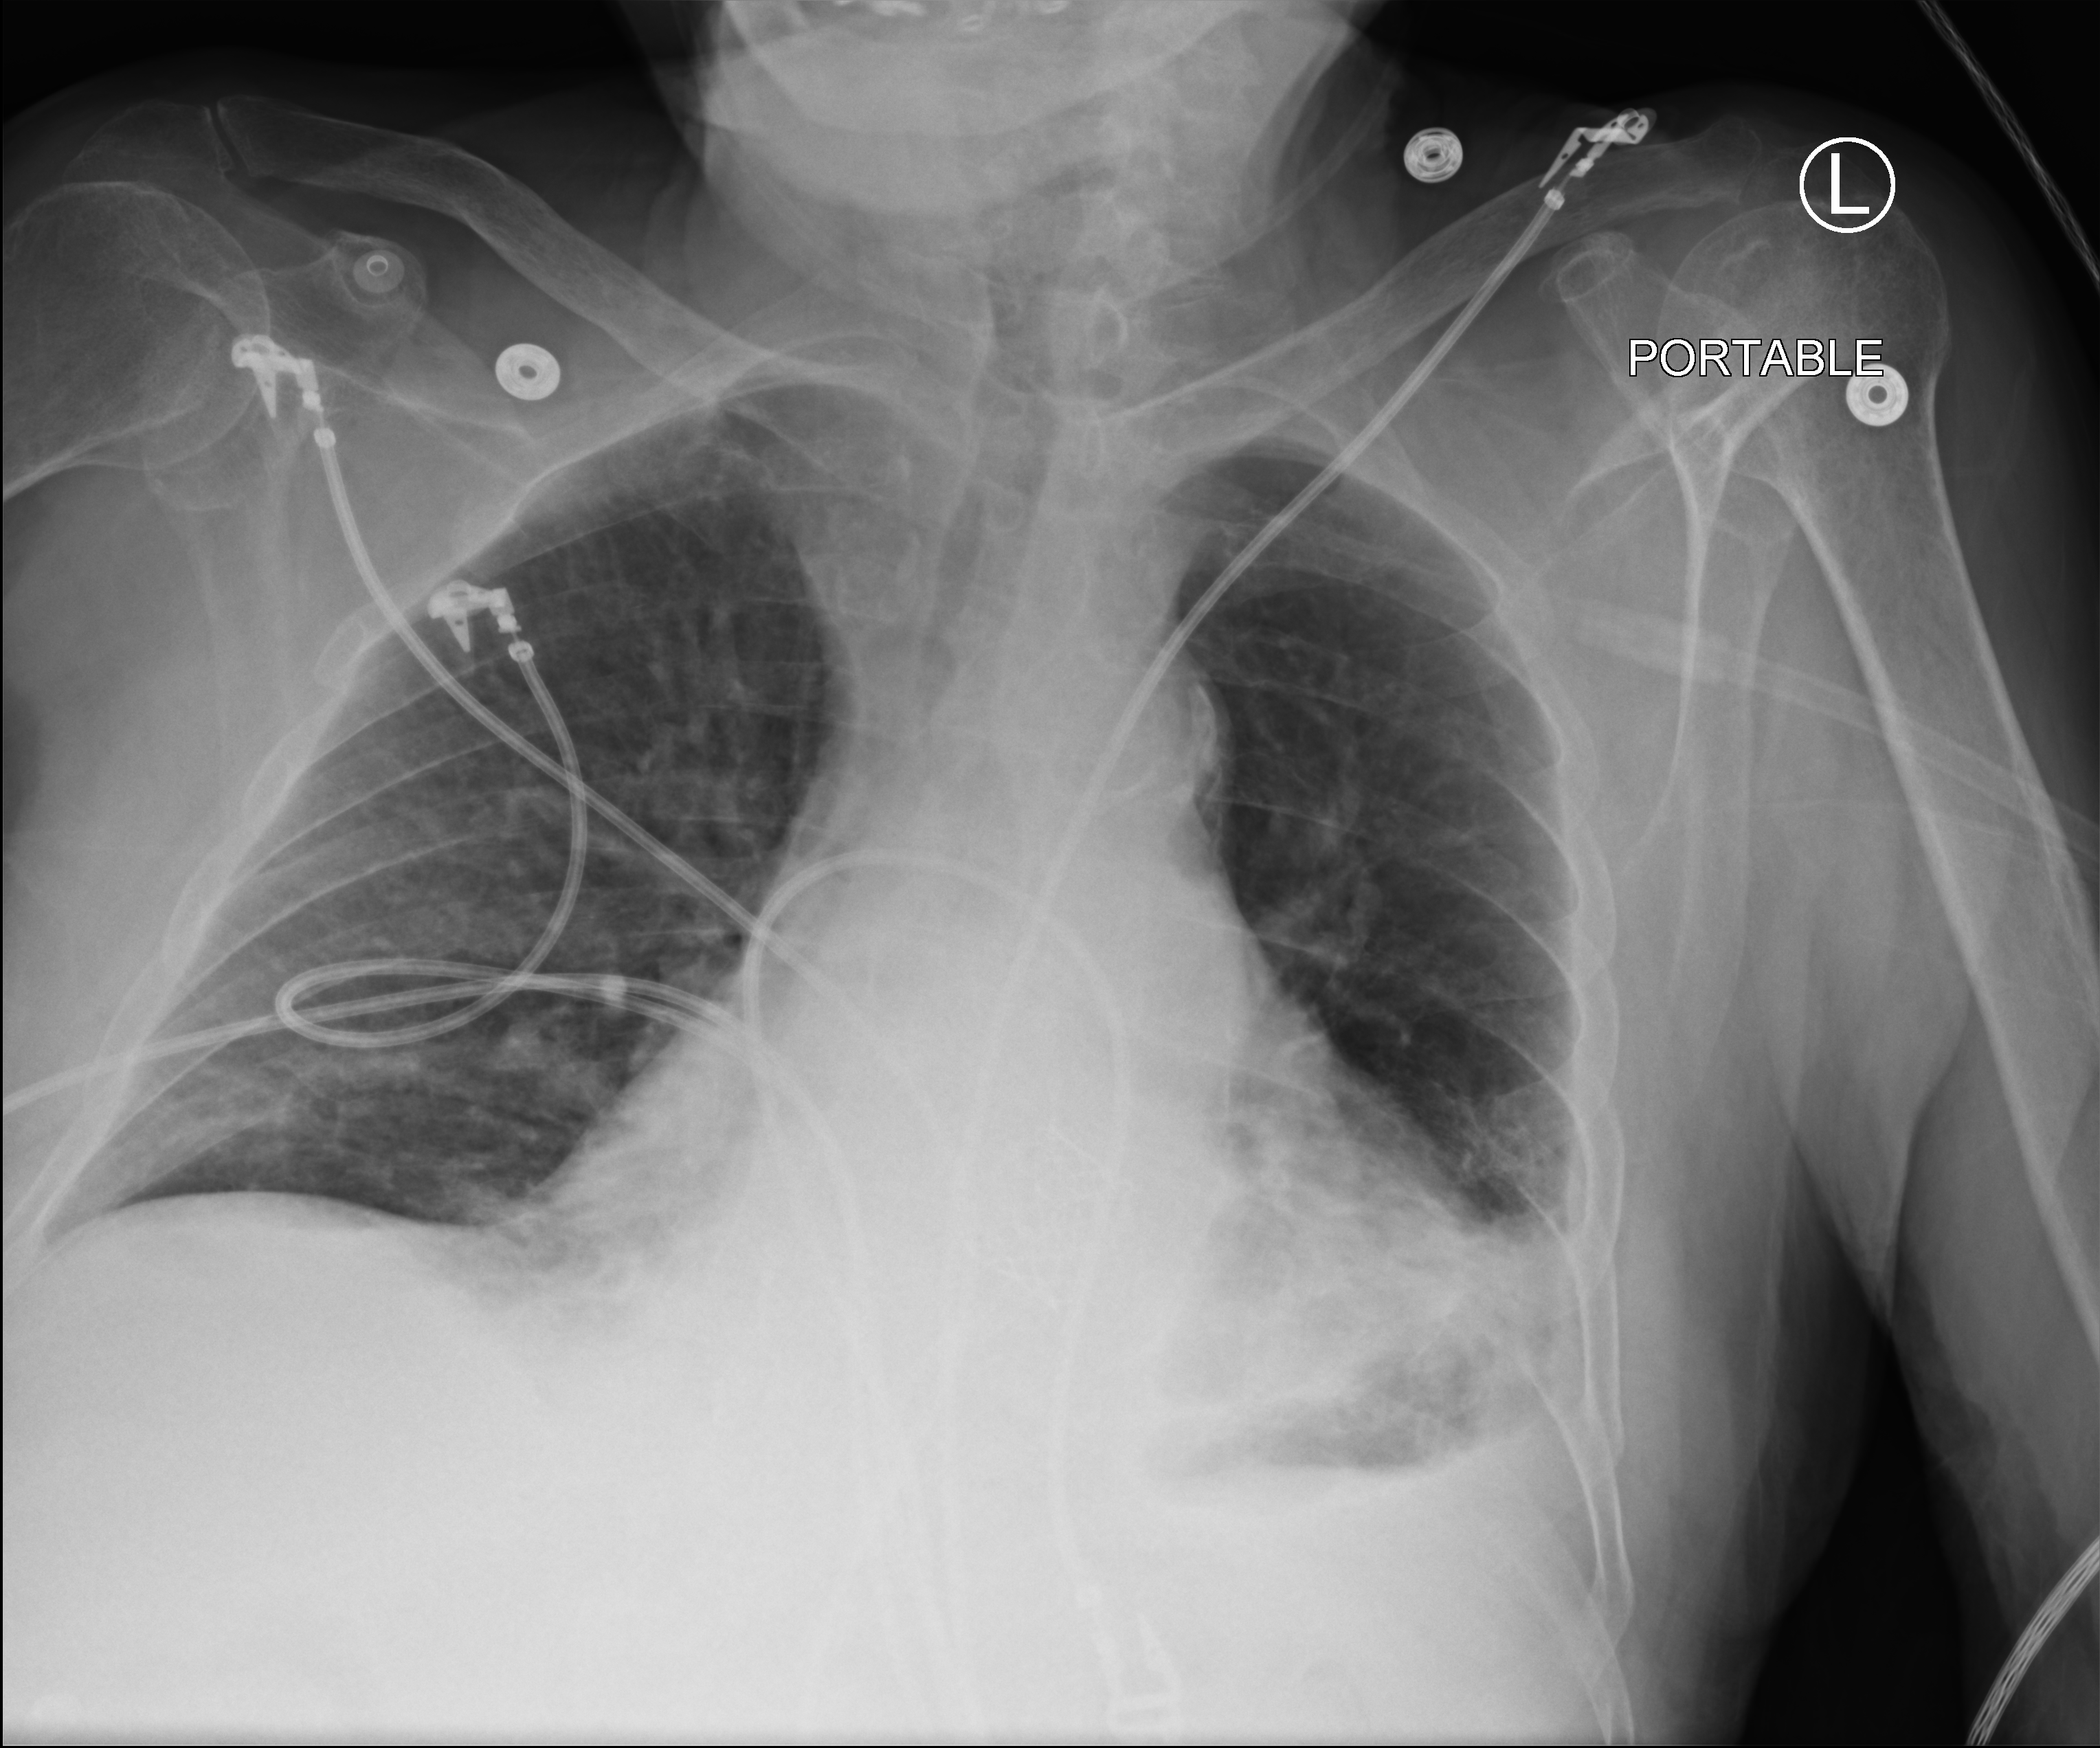
Chest X-ray (portable). Patient hospitalised with COVID-19; male, aged 75–90 years.
Hospital-stay facts (about this admission, not read from this image; timing relative to this image not recorded): admitted to intensive care during this hospital stay: yes; mechanically ventilated during this hospital stay: no; smoking status (admission record): former.